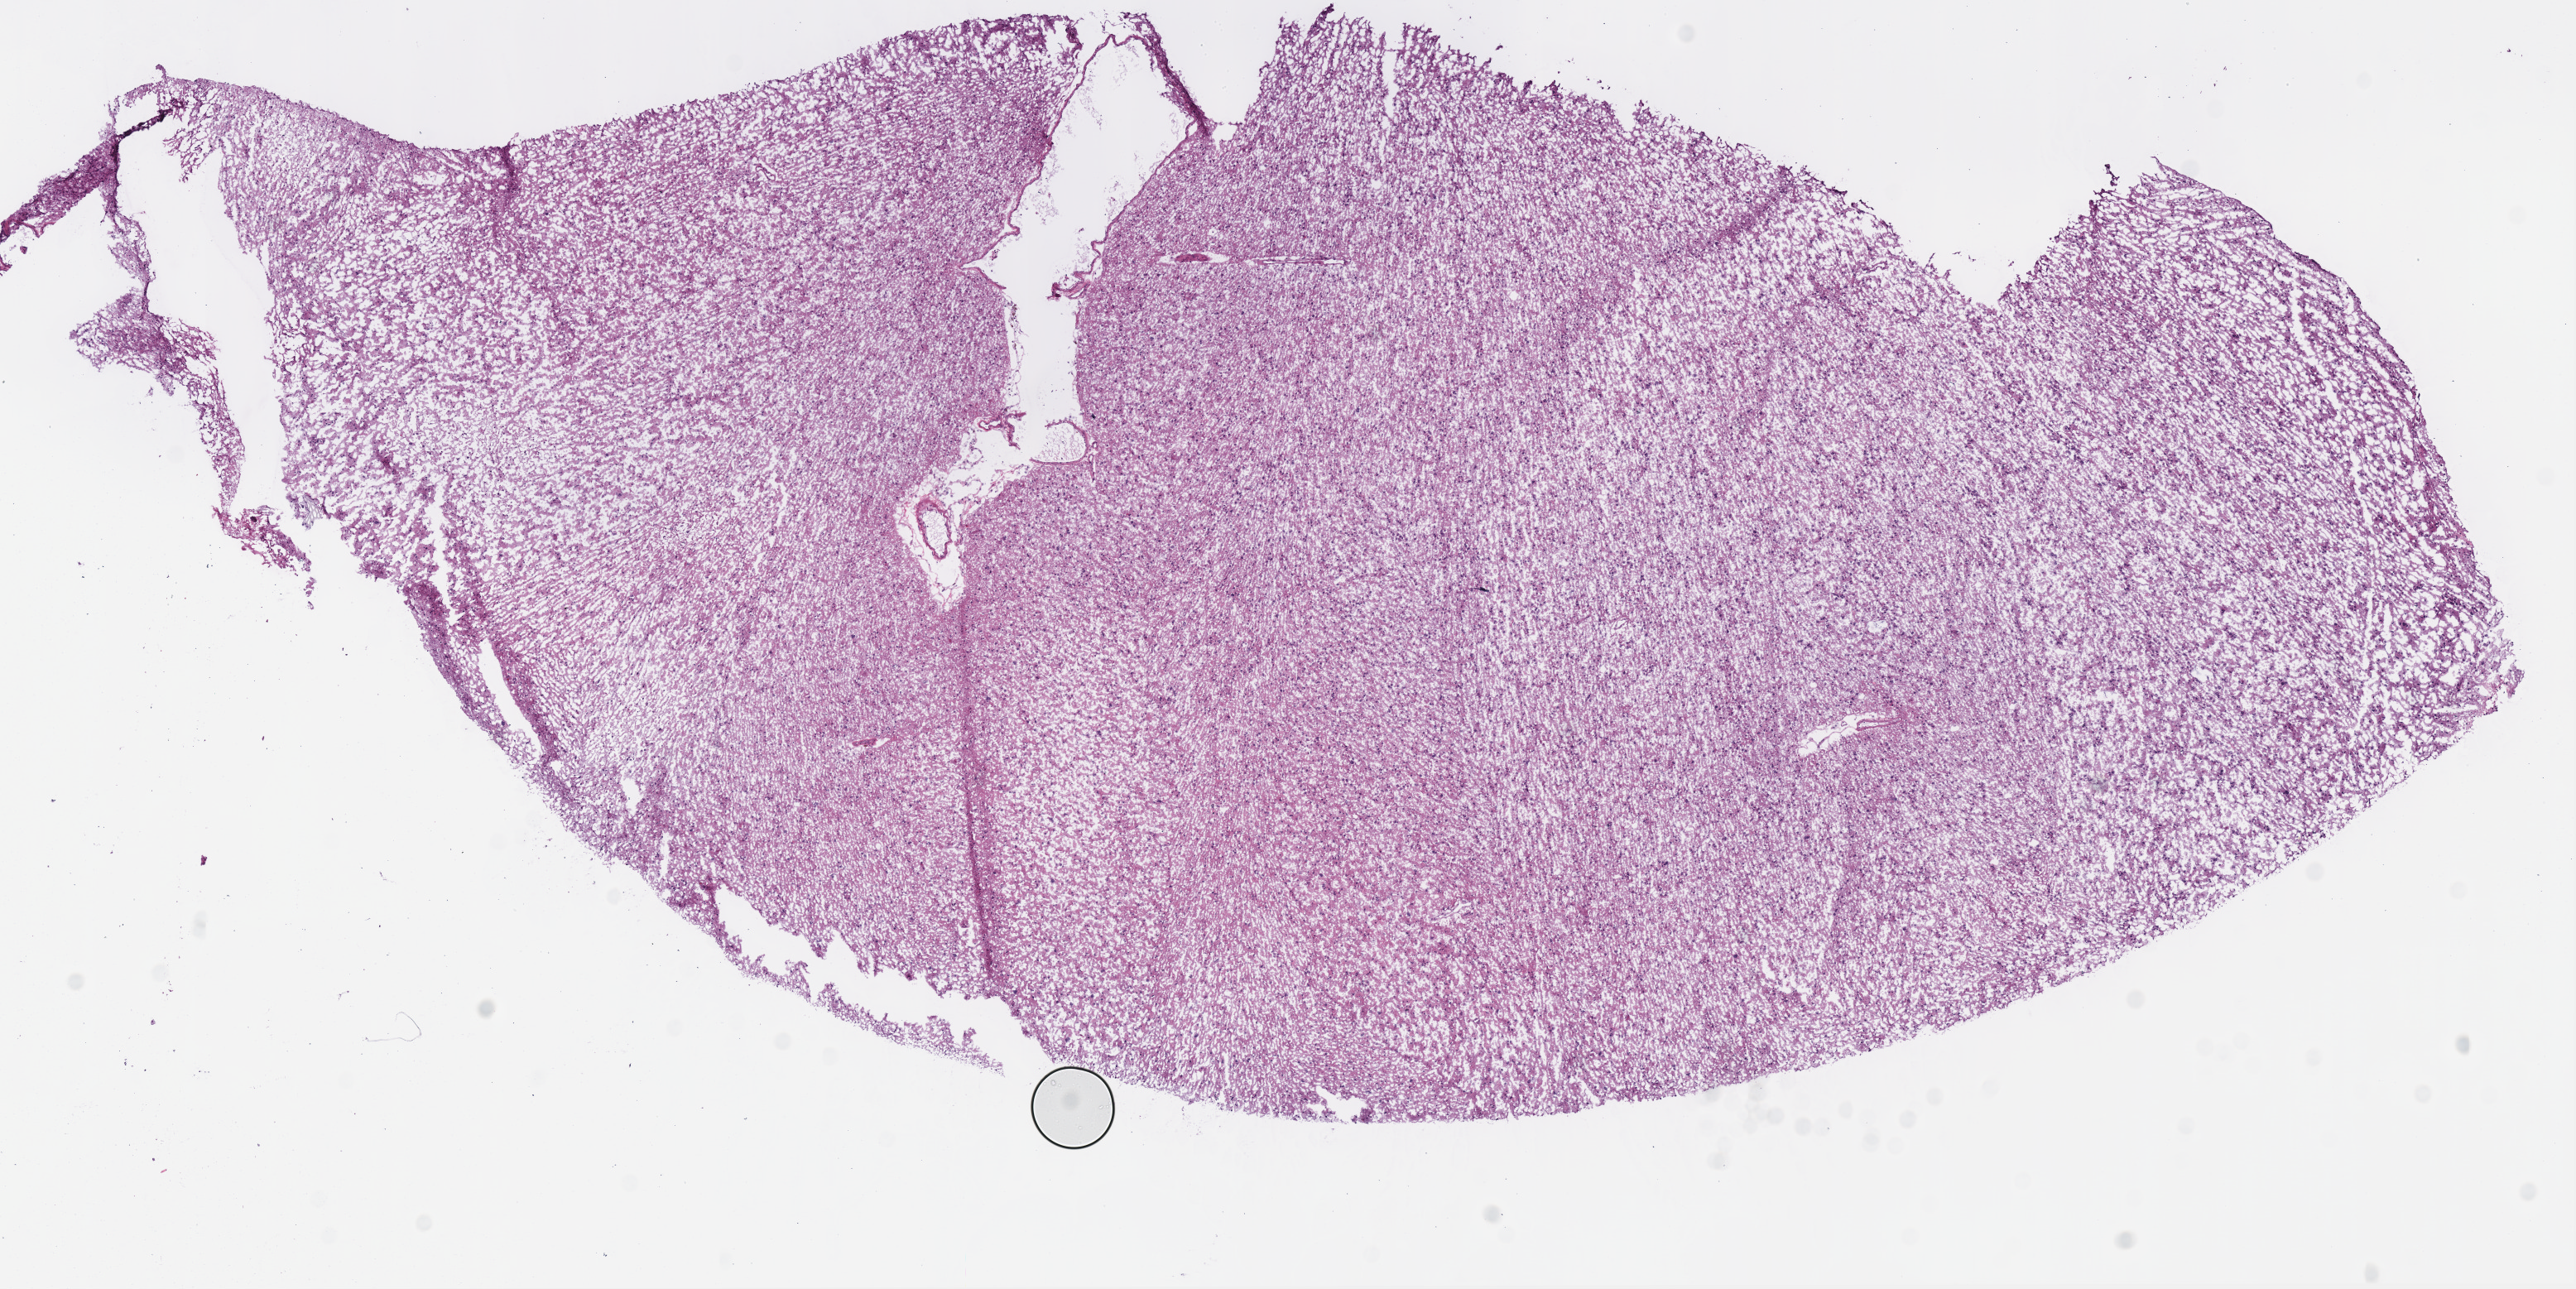
Whole-slide histology image, Hematoxylin and eosin (H&E) stained — a low-resolution overview of the entire scanned area, about 12.2 x 6.1 mm (from a 40x scan). Frozen section. Brain, primary tumour sample. Male patient; age at initial diagnosis 41 years. Histologic grade: G2 (moderately differentiated). Pathologist review of this section (percent, as recorded): tumour cells 100%, tumour nuclei 75%, normal cells 0%, stromal cells 0%, necrosis 0%.
- pathologic diagnosis: Mixed glioma (cerebrum)
- laterality: left